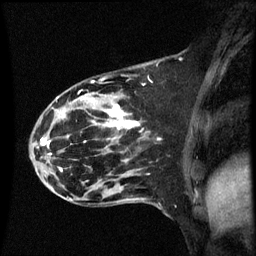
Breast MRI (dynamic contrast-enhanced), one sagittal slice. Slice 21 of 60 in the series (ordered by position). Dynamic contrast-enhanced series, image 2 of 3 at this slice position (ordered by acquisition). 1.5 T. TE 4.2 ms, TR 8.9 ms. 2 mm slice thickness. 256 × 256 image matrix, field of view 200 × 200 mm. Female patient, age 44 years. Case-level facts recorded for this patient, not image findings: setting: breast cancer imaged before/during neoadjuvant chemotherapy; receptor status: HR-positive, HER2-negative.
Structures marked on this image (semi-automatic segmentation, software-assisted and operator-edited):
- analysis volume of interest (the breast-tissue region the enhancement analysis was run in; not a lesion): bounding box [x1, y1, x2, y2] px = [43, 80, 151, 189]
- tumour enhancement mask (voxels above the 70 % enhancement threshold inside the analysis volume of interest): [109, 106, 139, 129]